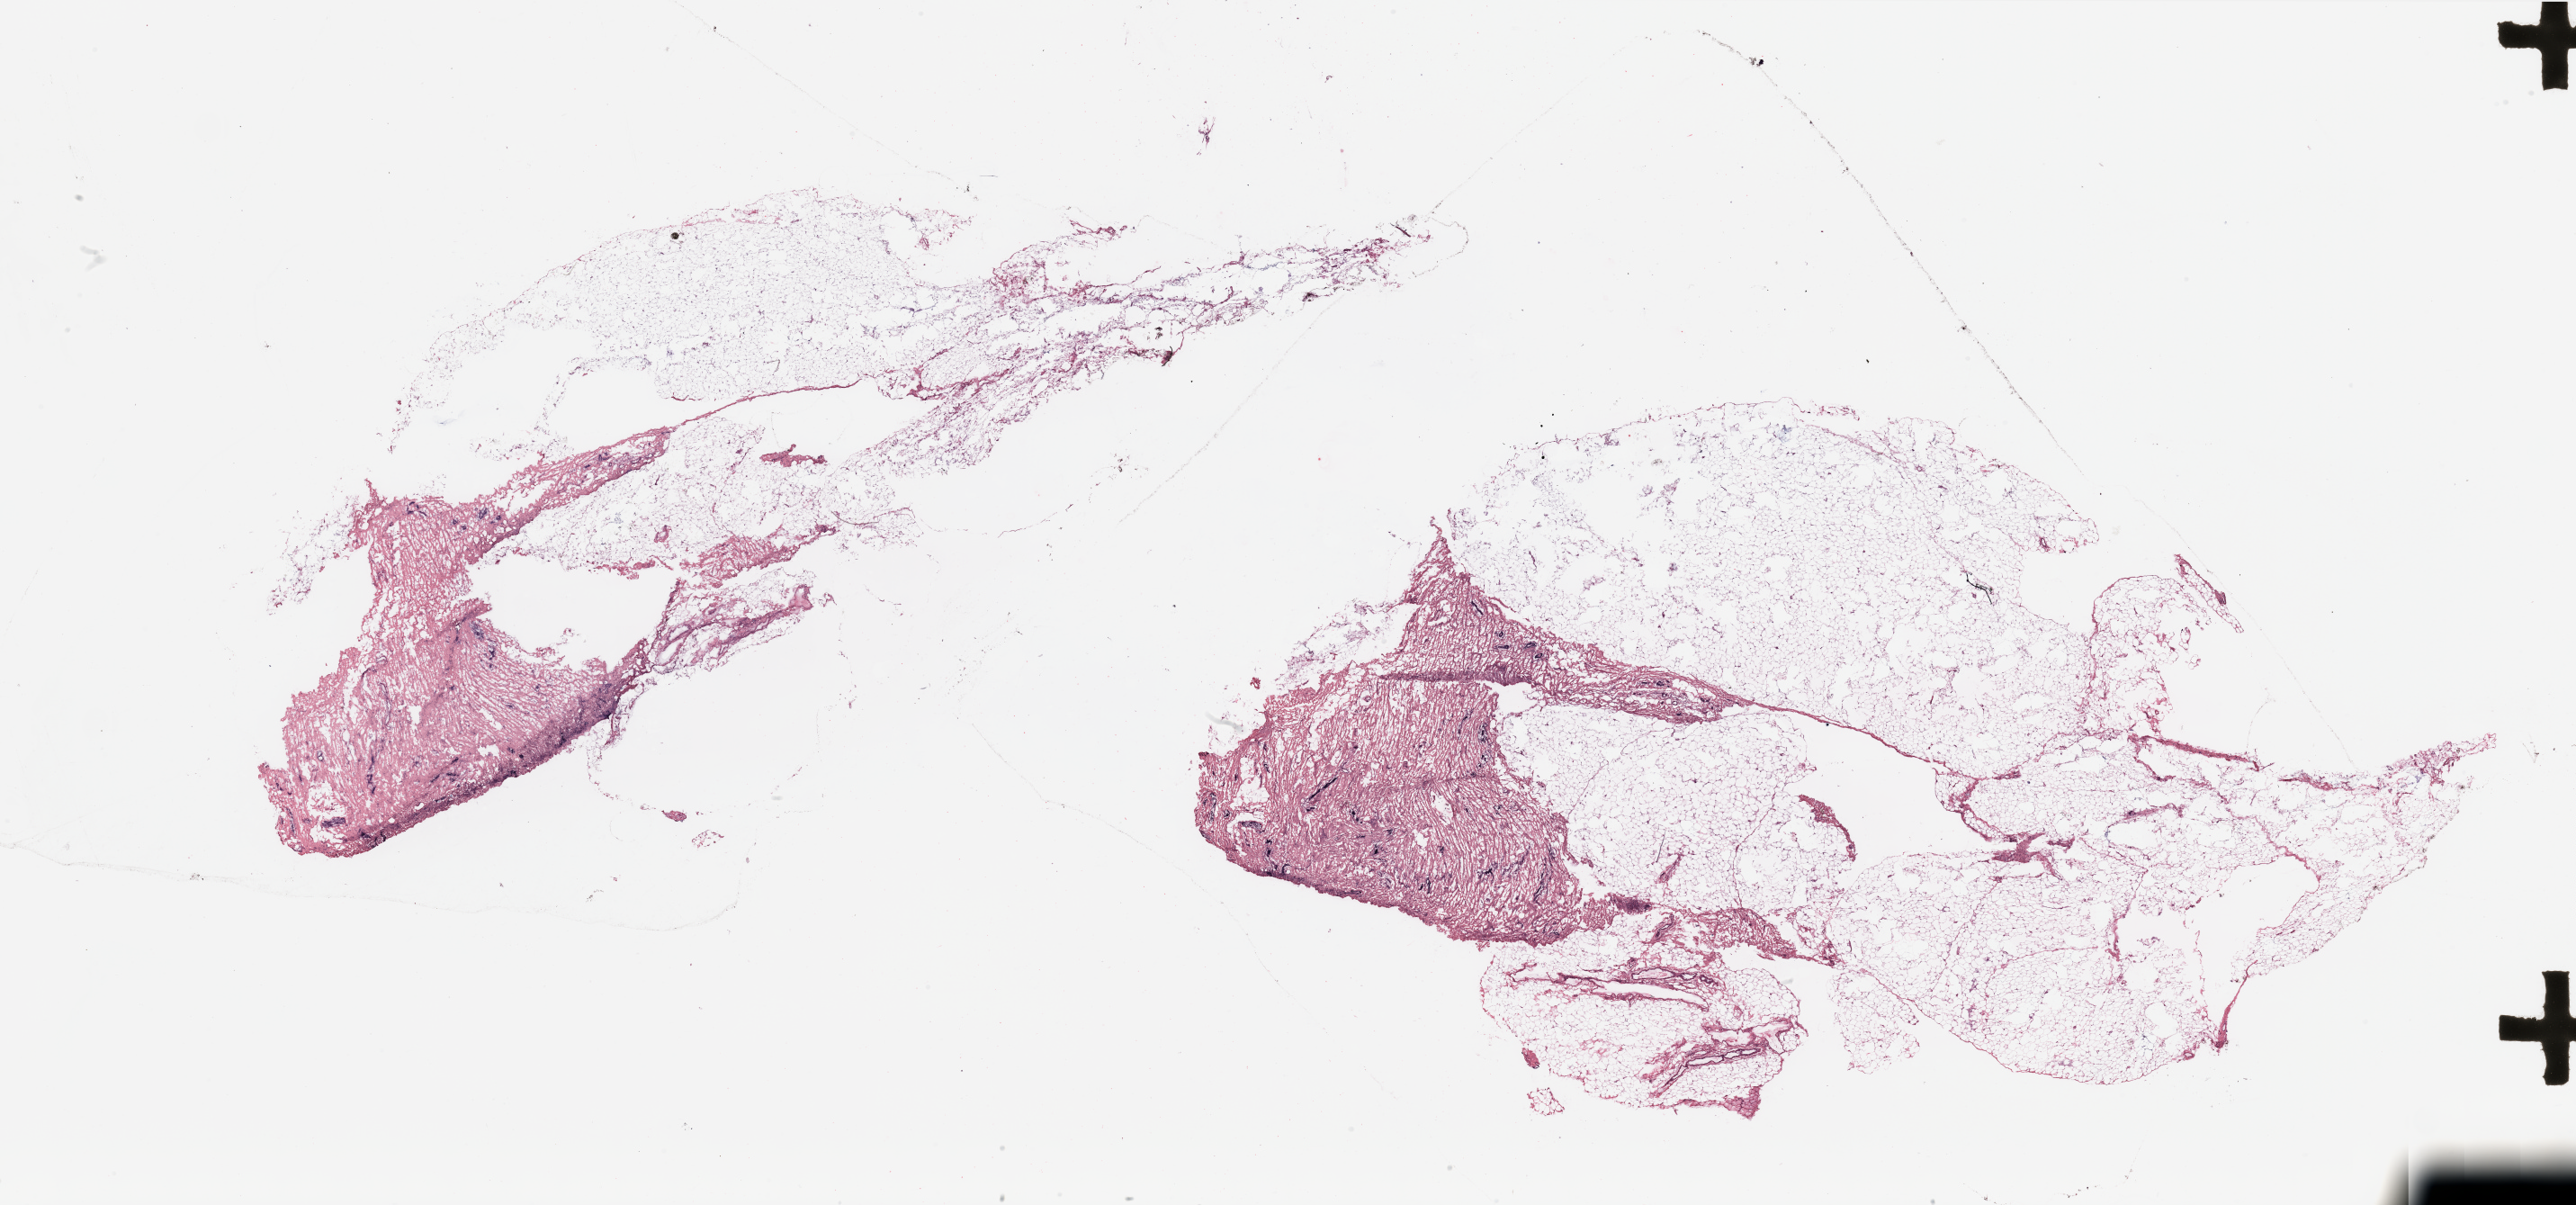
Whole-slide histology image, H&E, a low-resolution overview of the entire scanned area, about 45.3 x 21.2 mm, breast, tumour tissue. Female, 67 y/o.
Histologic diagnosis: Infiltrating duct carcinoma, NOS.